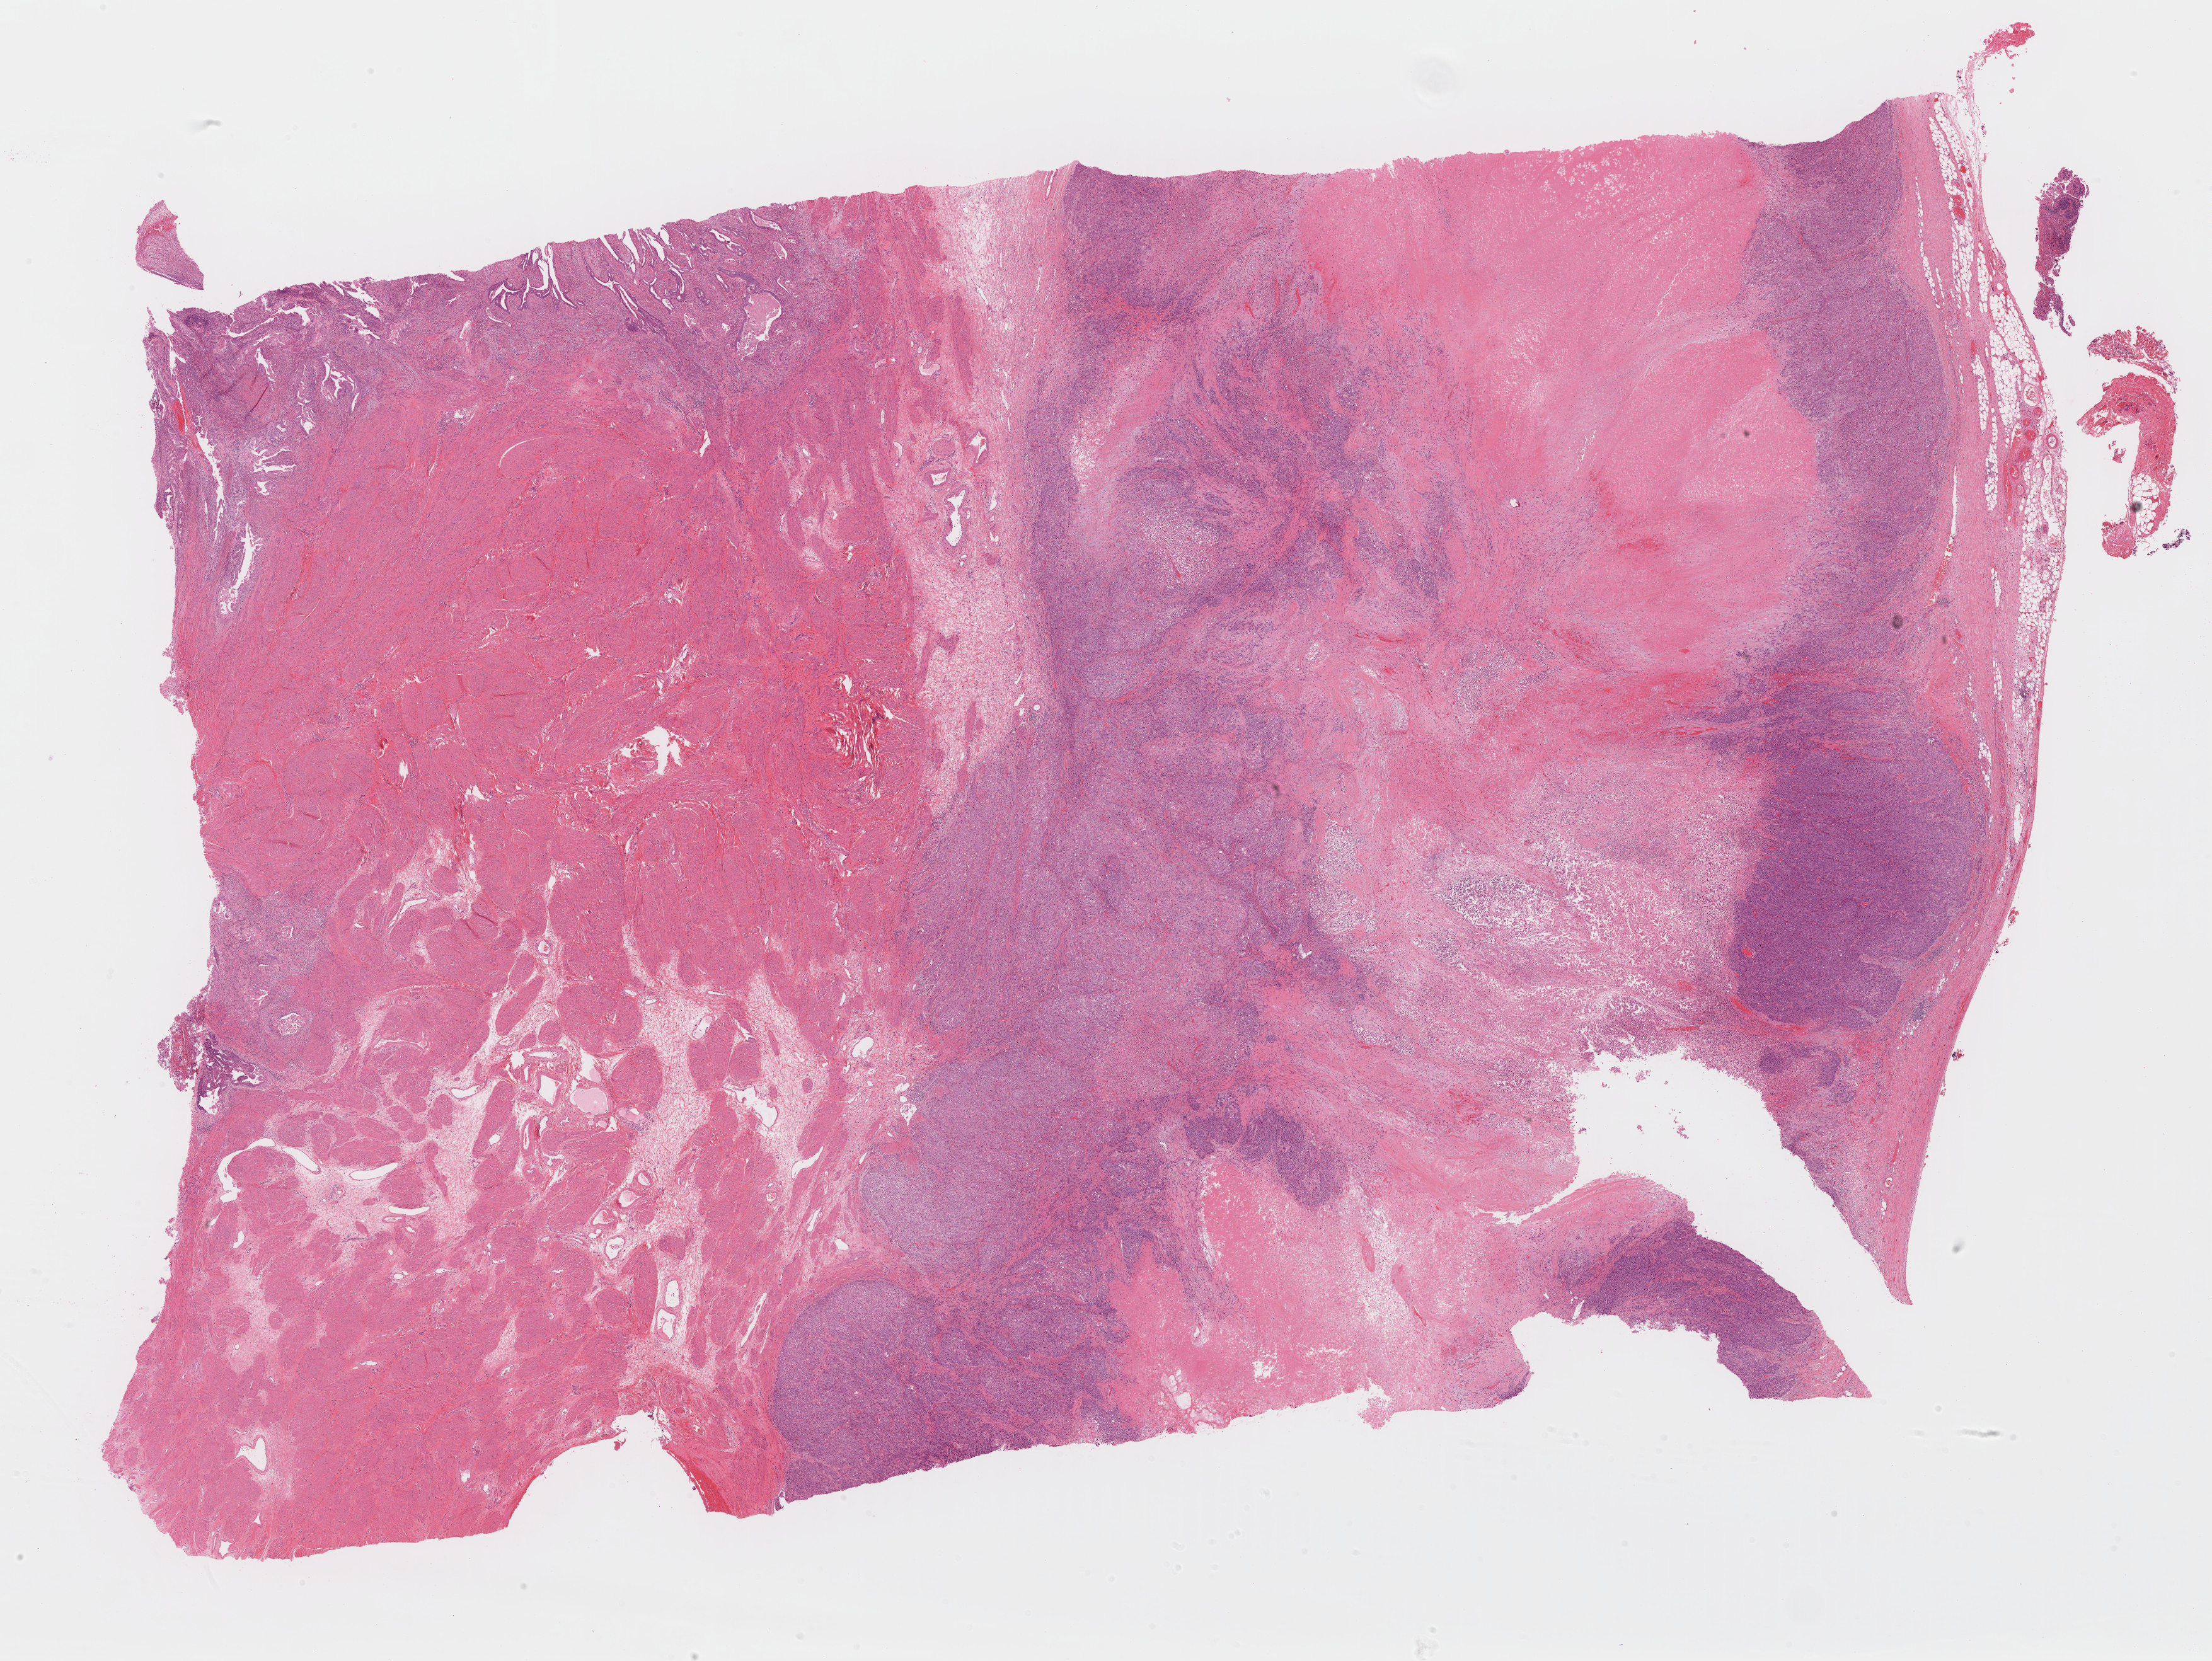
Whole-slide histology image, H&E-stained — a low-resolution overview of the entire scanned area, about 27.7 x 20.8 mm (from a 40x scan); formalin-fixed paraffin-embedded (FFPE) diagnostic section; uterus, primary tumour sample. Female, age 56 years at initial diagnosis. Histologic grade: G3 (poorly differentiated).
Lymph nodes positive (case pathology): 1 of 2 examined. FIGO stage: IVB. Histologic diagnosis: Endometrioid adenocarcinoma, NOS (endometrium).